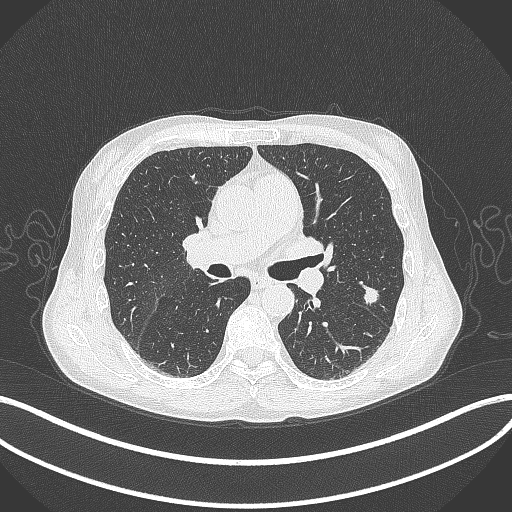
Chest CT, one axial slice. Position 209 of 429 along the scan axis. Lung window (W 1500 / L -600 HU). 1 mm slice thickness. 512 × 512 image matrix. Patient: male, 58 years. Case-level facts recorded for this patient, not image findings: clinical TNM (as recorded): T1c N0 M0; histopathological grade: G2.
Outlined on this slice (rectangle marked by the reading radiologist):
- lung tumour (recorded histology: adenocarcinoma): bounding box (x1, y1, x2, y2) in pixels: (362, 285, 381, 304)